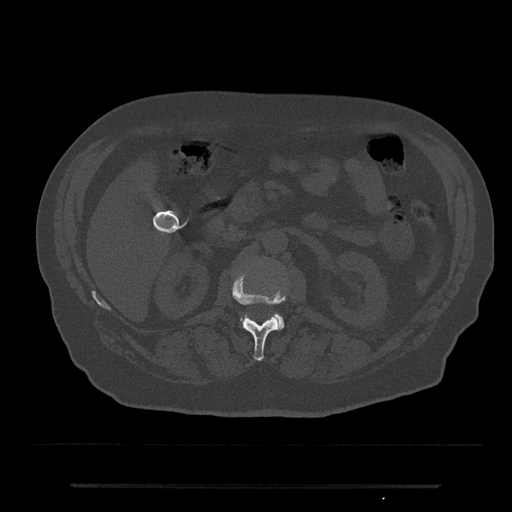
CT including the spine, one axial slice. Slice 516 of 797 in the series (ordered by position). Reconstruction kernel Br40s/3. 120 kVp. Bone window (W 1800 / L 400 HU). 0.5 mm slice thickness. 512 × 512 image matrix, field of view 434 × 434 mm. Patient: male, 80 years. Case-level facts recorded for this patient, not image findings: primary cancer: prostate.
Structures marked on this image (semi-automatic segmentation, software-assisted and operator-edited):
- L1 vertebra: bounding box (x1, y1, x2, y2) in pixels: (232, 274, 285, 361)
- L2 vertebra: (240, 313, 285, 330)